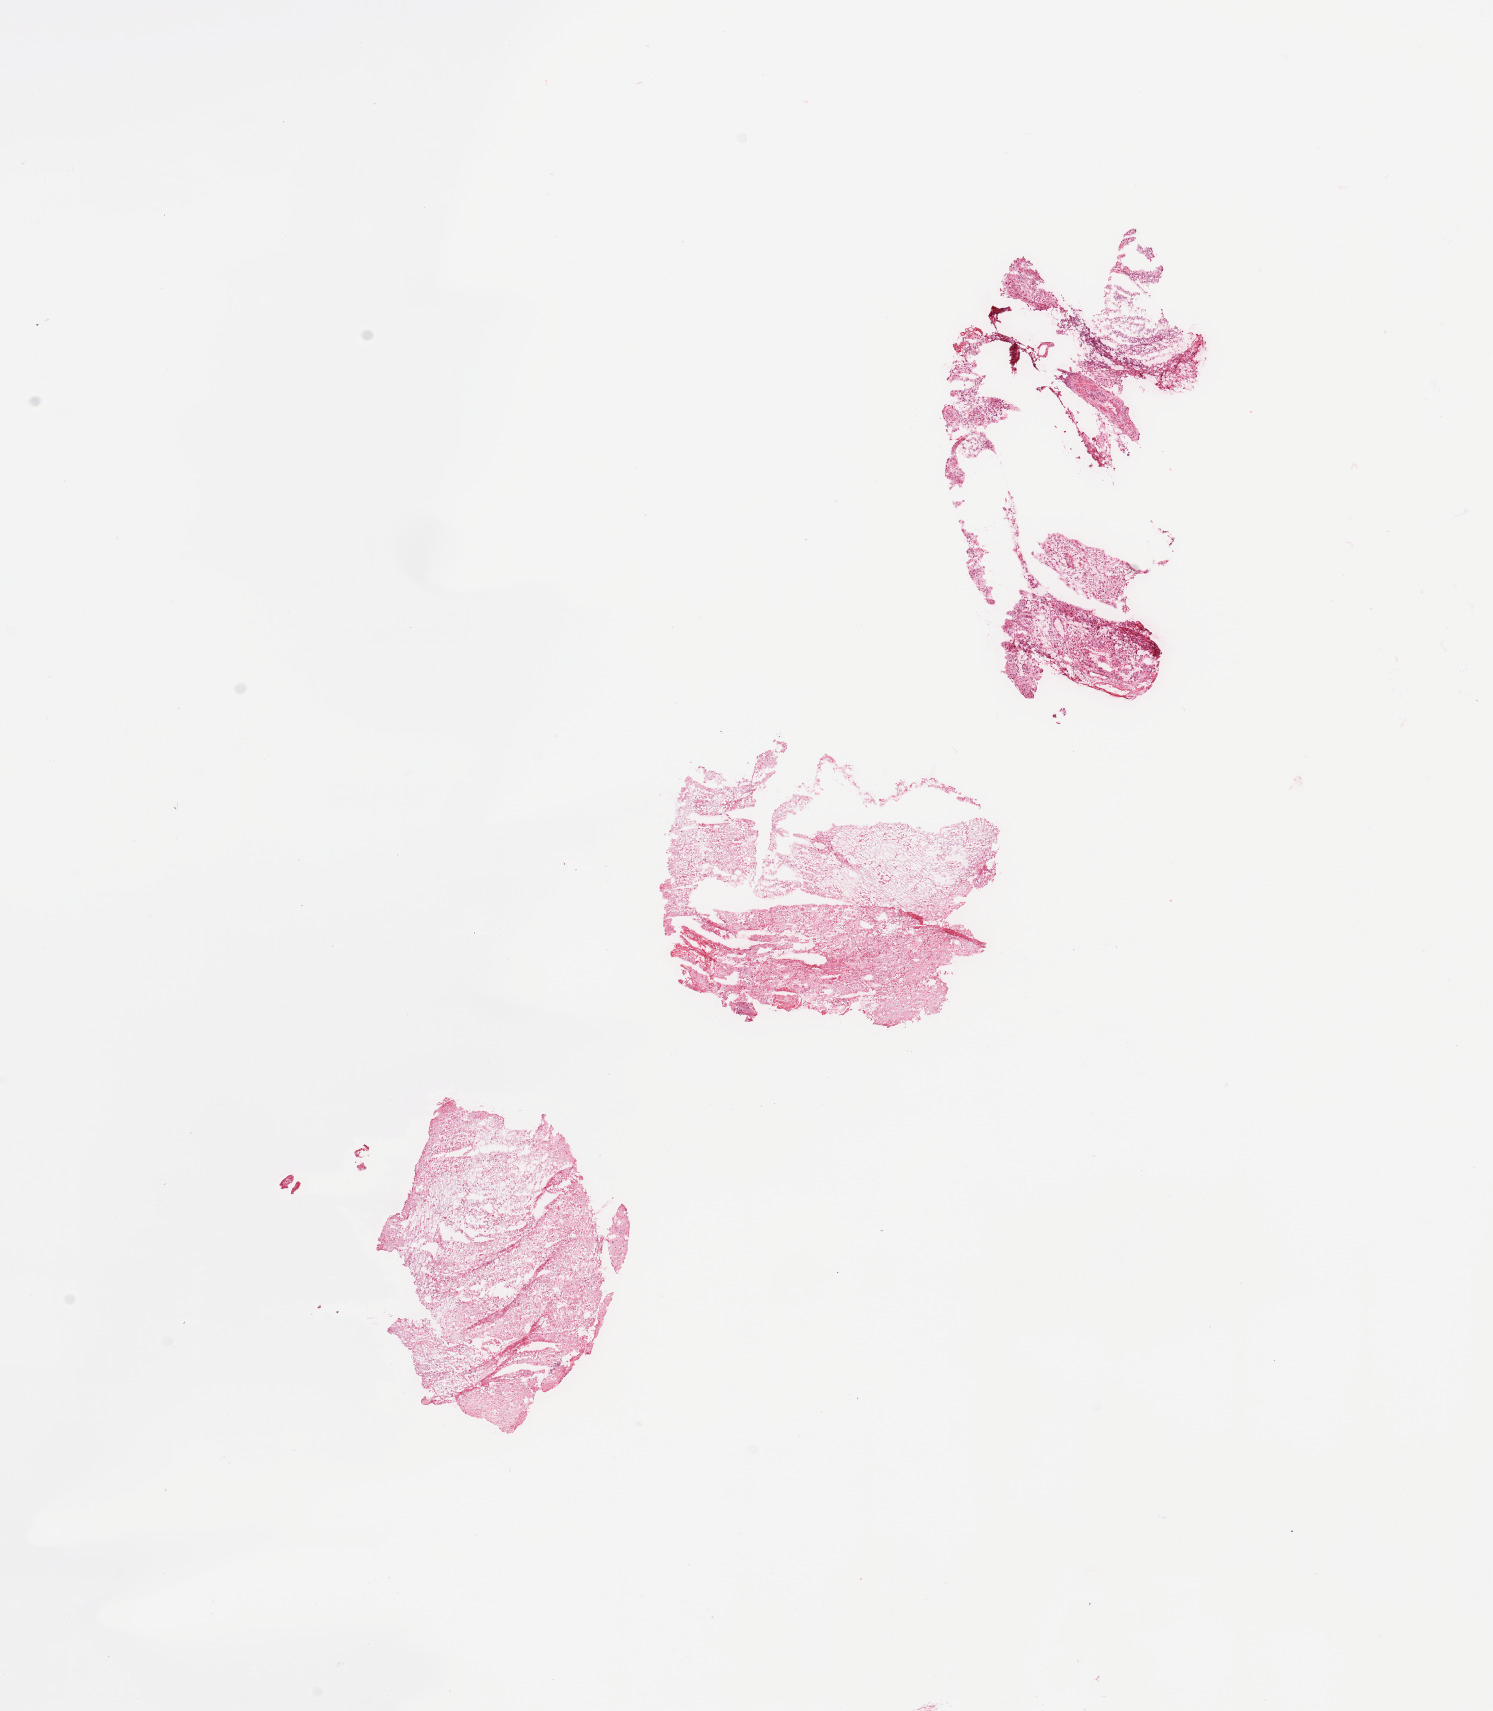
Digitized Hematoxylin and eosin (H&E) stained tissue section (whole slide), shown as a low-resolution overview of the whole scanned area (about 11.8 x 13.5 mm). Tumour tissue sample, brain. Patient: male, age 68 years.
Patient diagnosis (cohort enrolment): glioblastoma multiforme (brain).